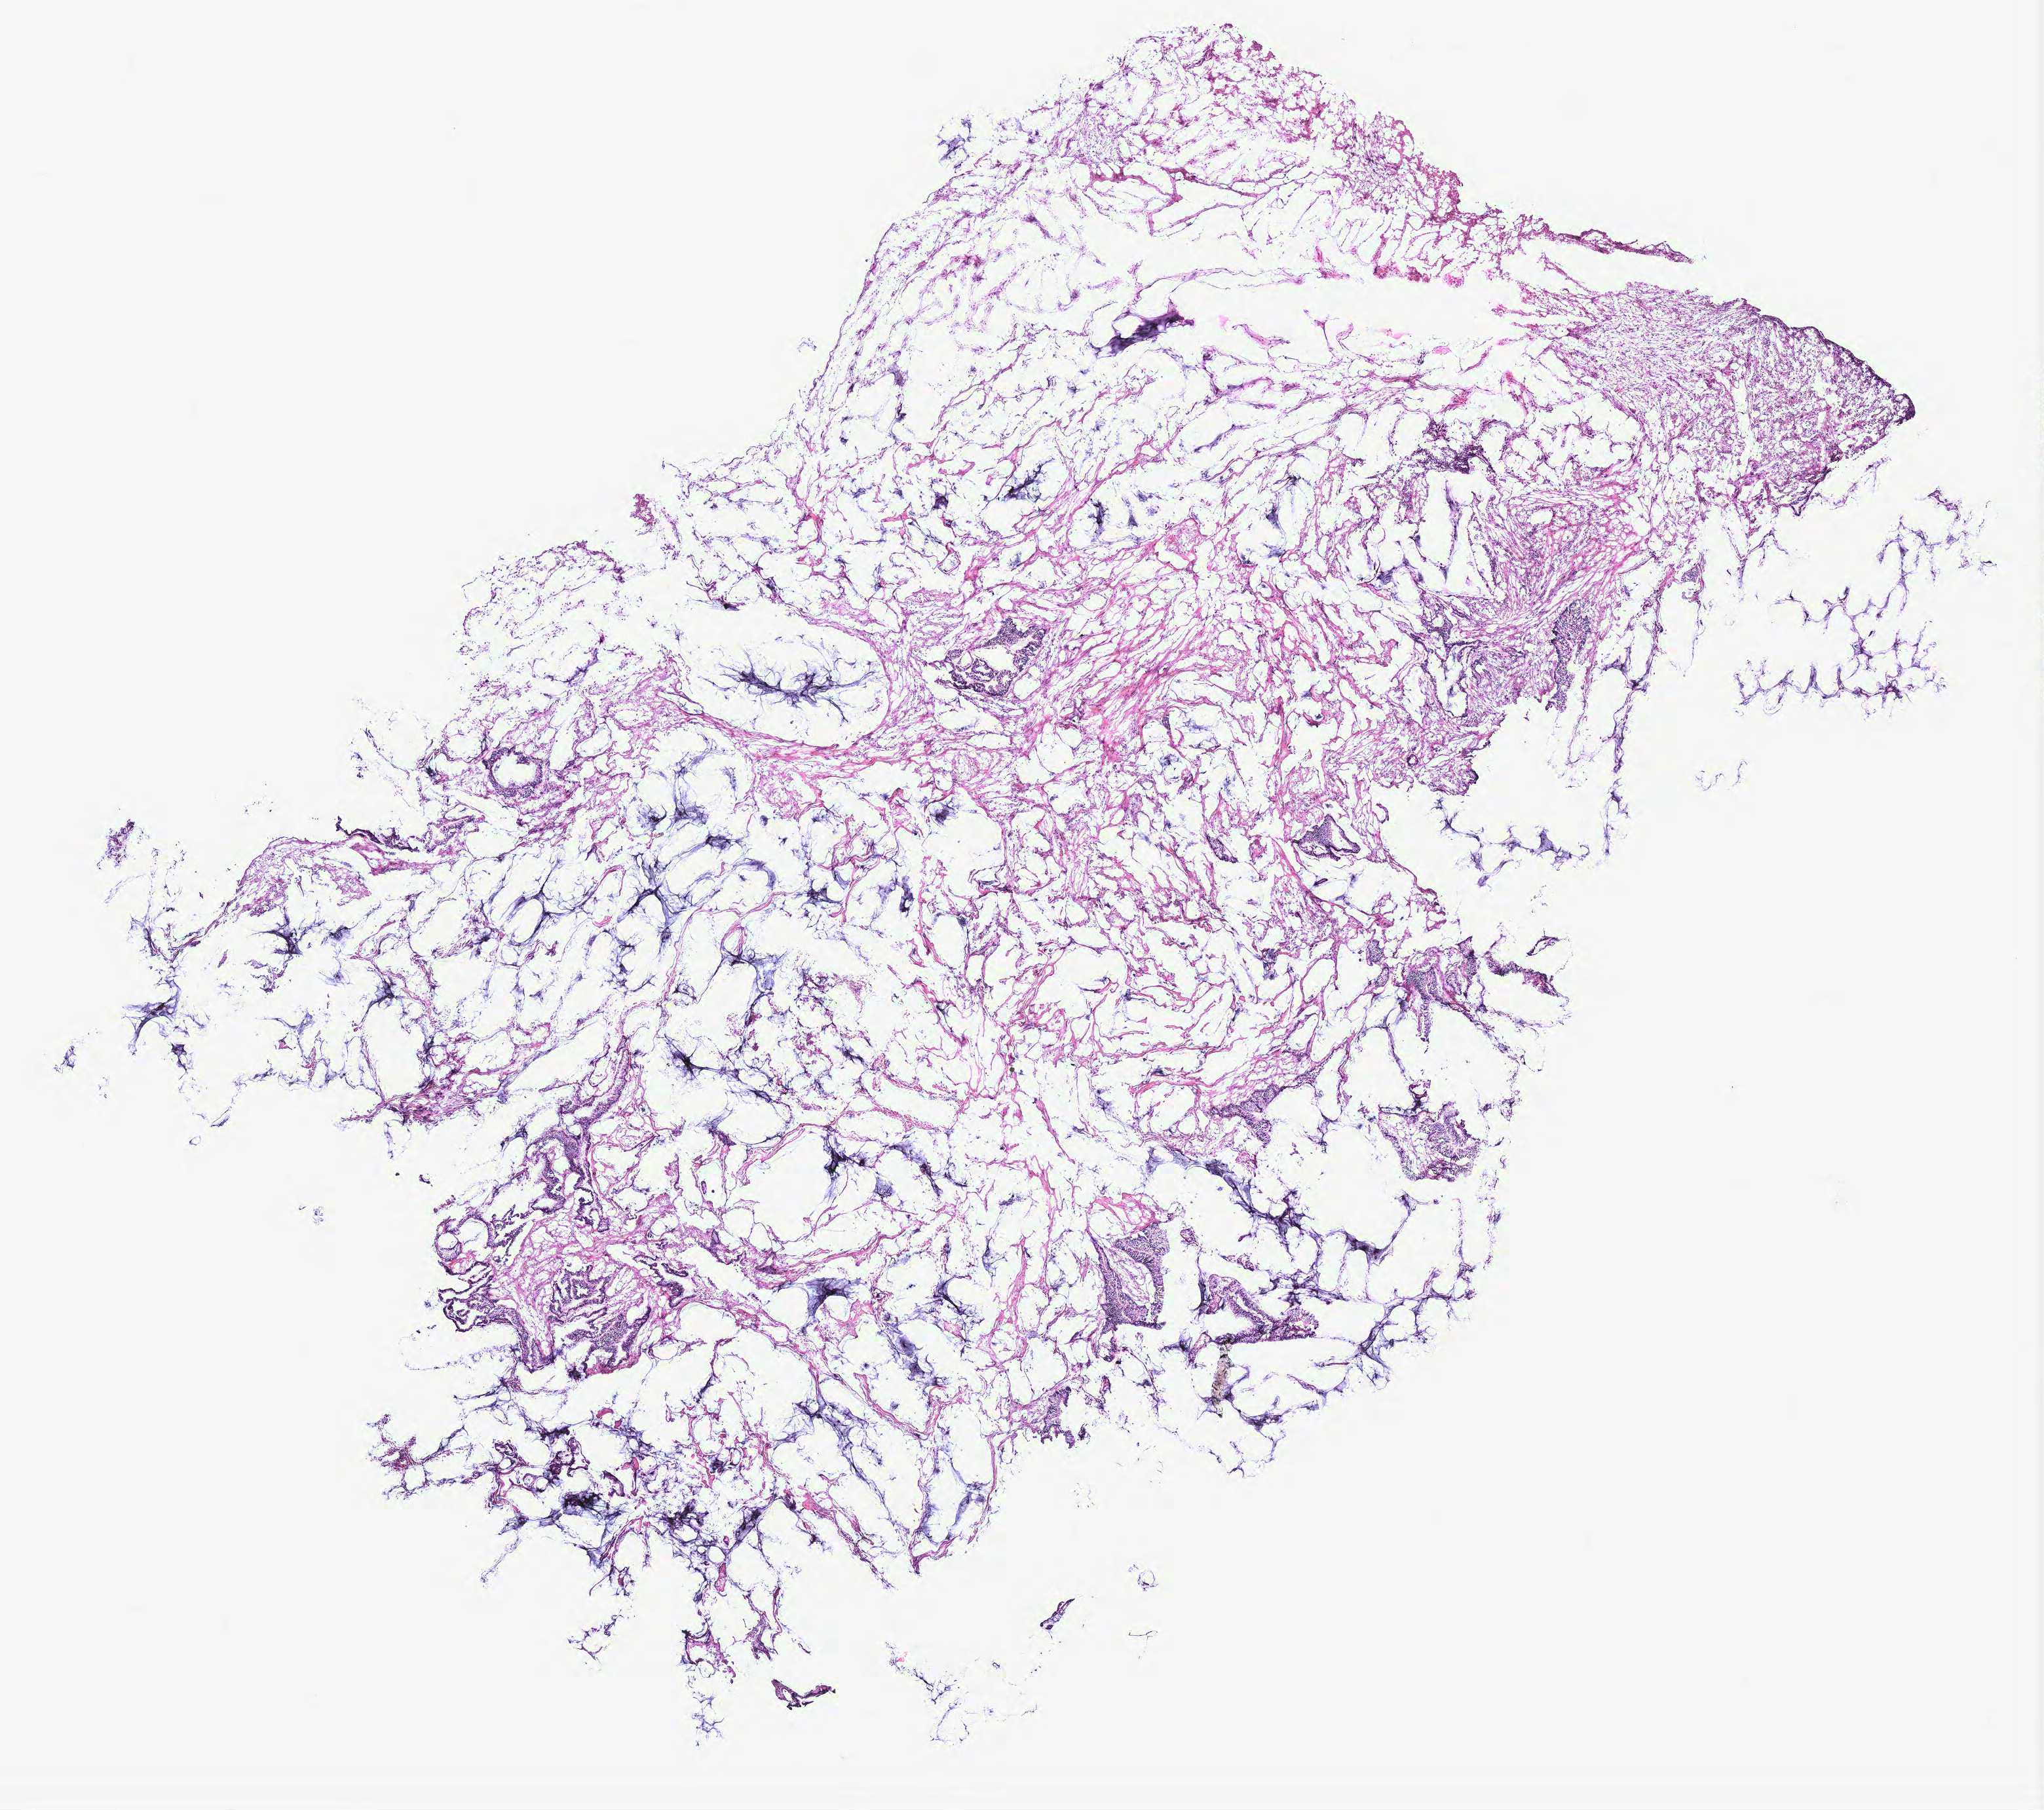
Digitized H&E tissue section (whole slide), a low-resolution overview of the entire scanned area, about 12.5 x 11.1 mm, colon, tissue type not recorded.
Patient diagnosis (cohort enrolment): colon cancer (colon).